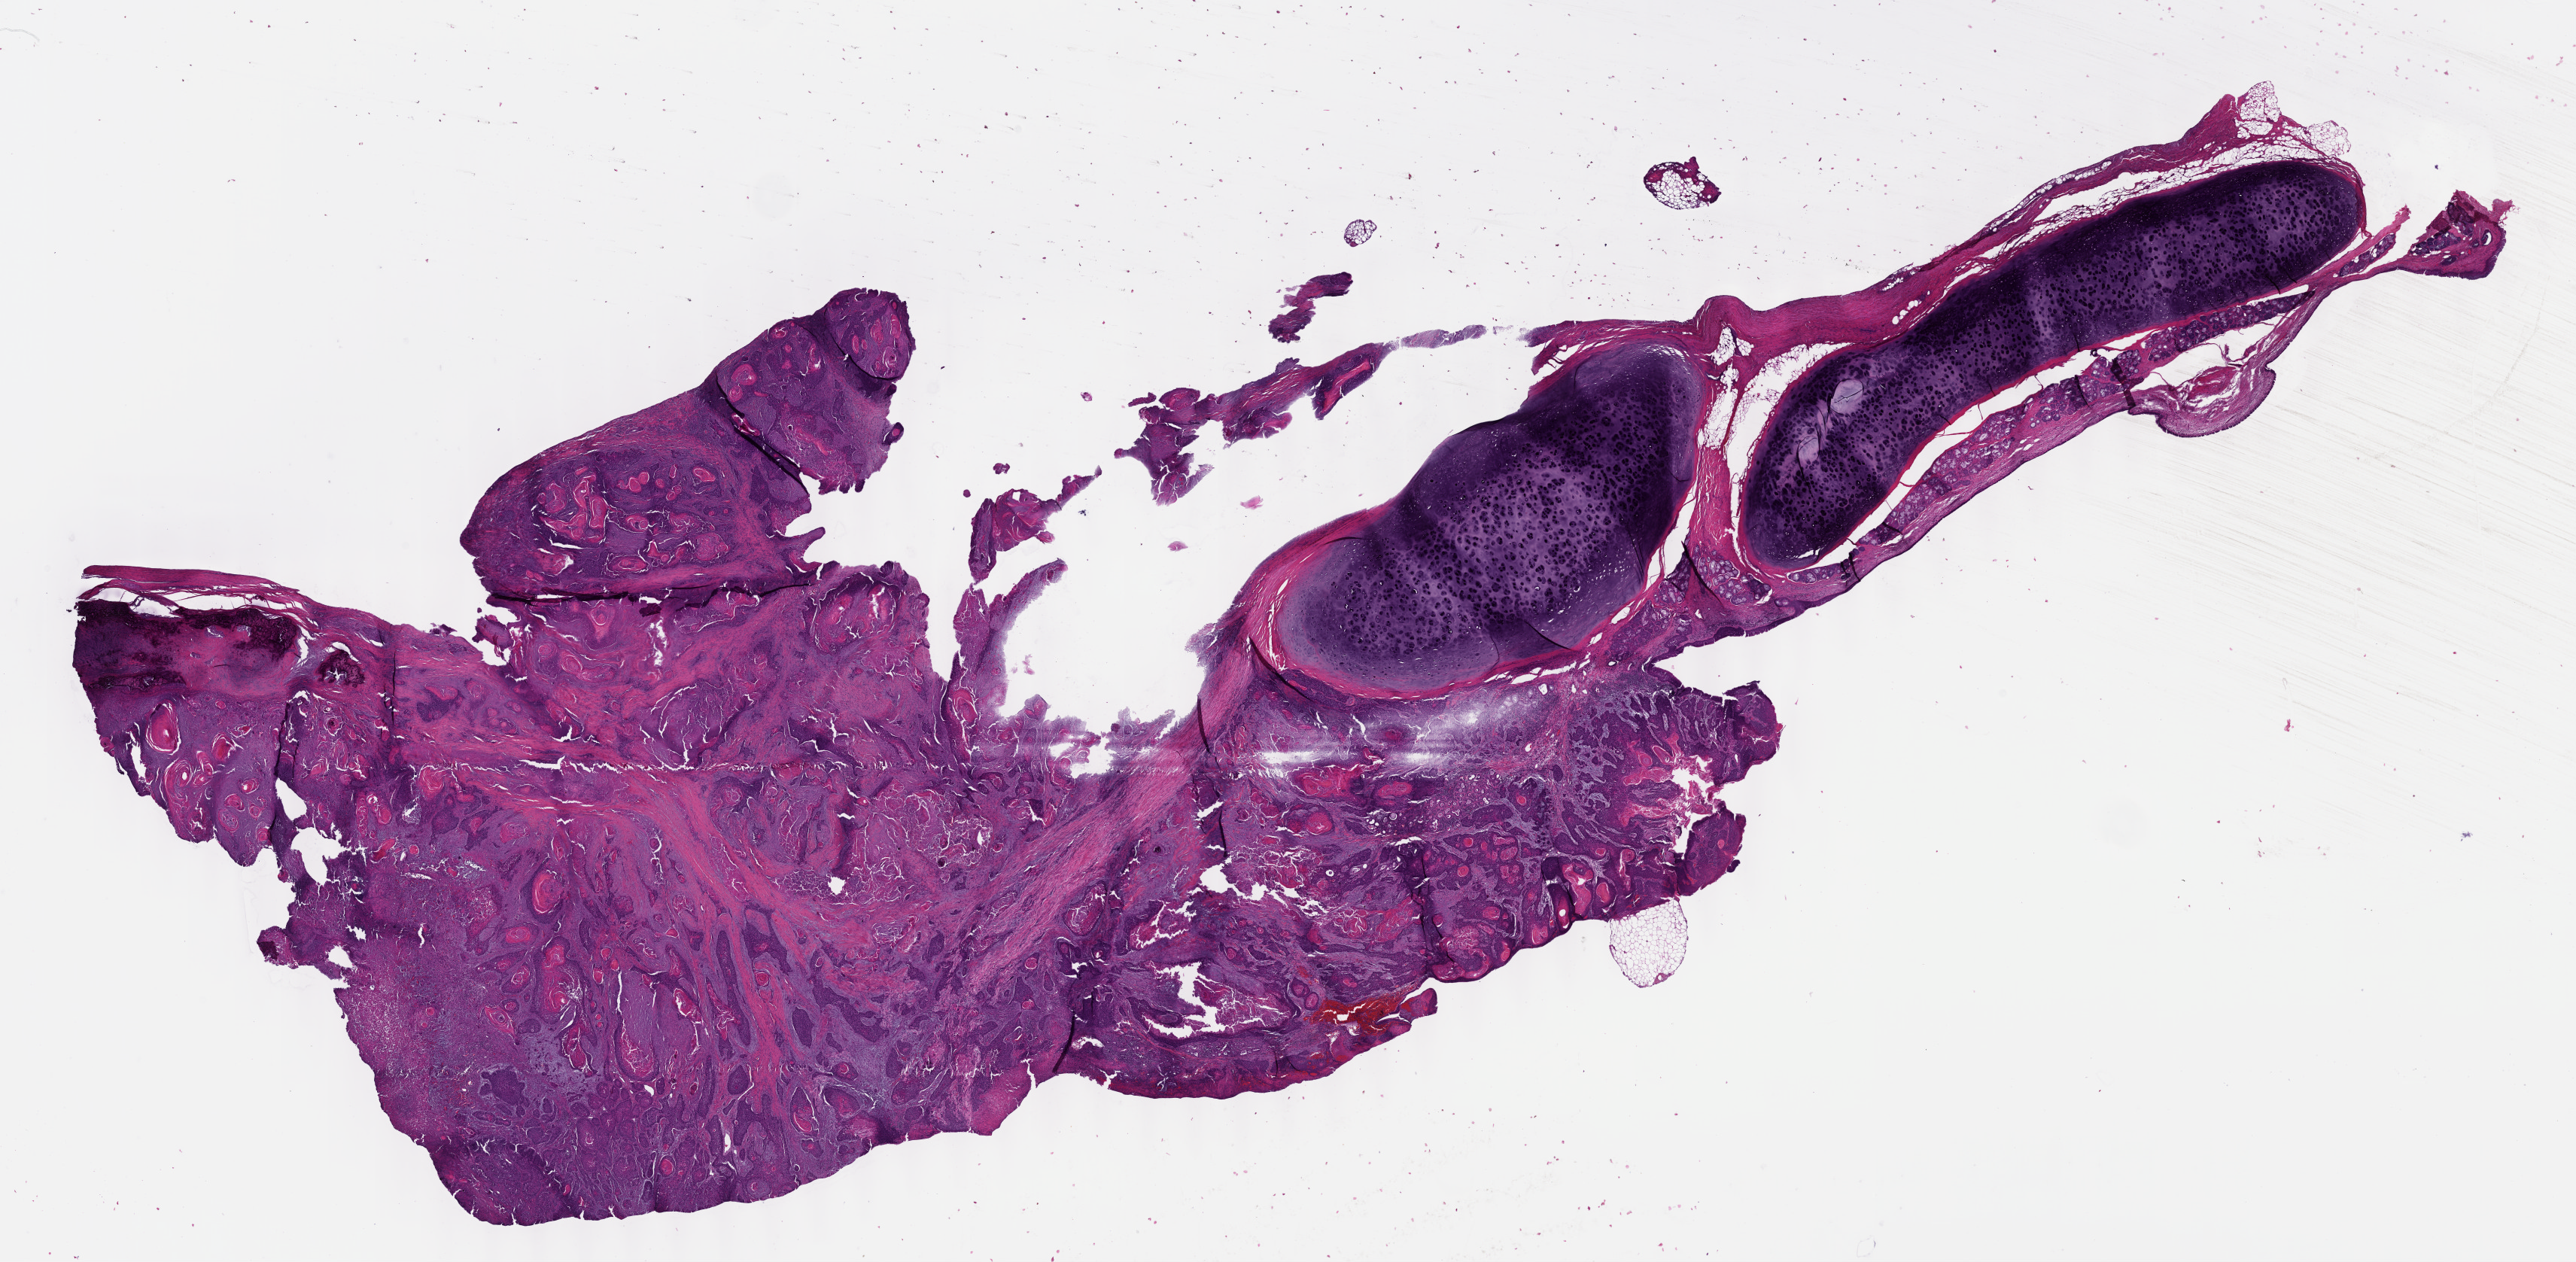
Whole-slide histology image, Hematoxylin and eosin (H&E) stained, whole scanned area (about 27.7 x 13.6 mm) shown as a low-resolution overview, FFPE section, primary tumour sample from the head and neck. Patient: male, age at initial diagnosis 57 years. Histologic grade: G2 (moderately differentiated).
Diagnosis: Squamous cell carcinoma, NOS (larynx, NOS). AJCC pathologic stage: IVA (7th edition). TNM: T4a N0.